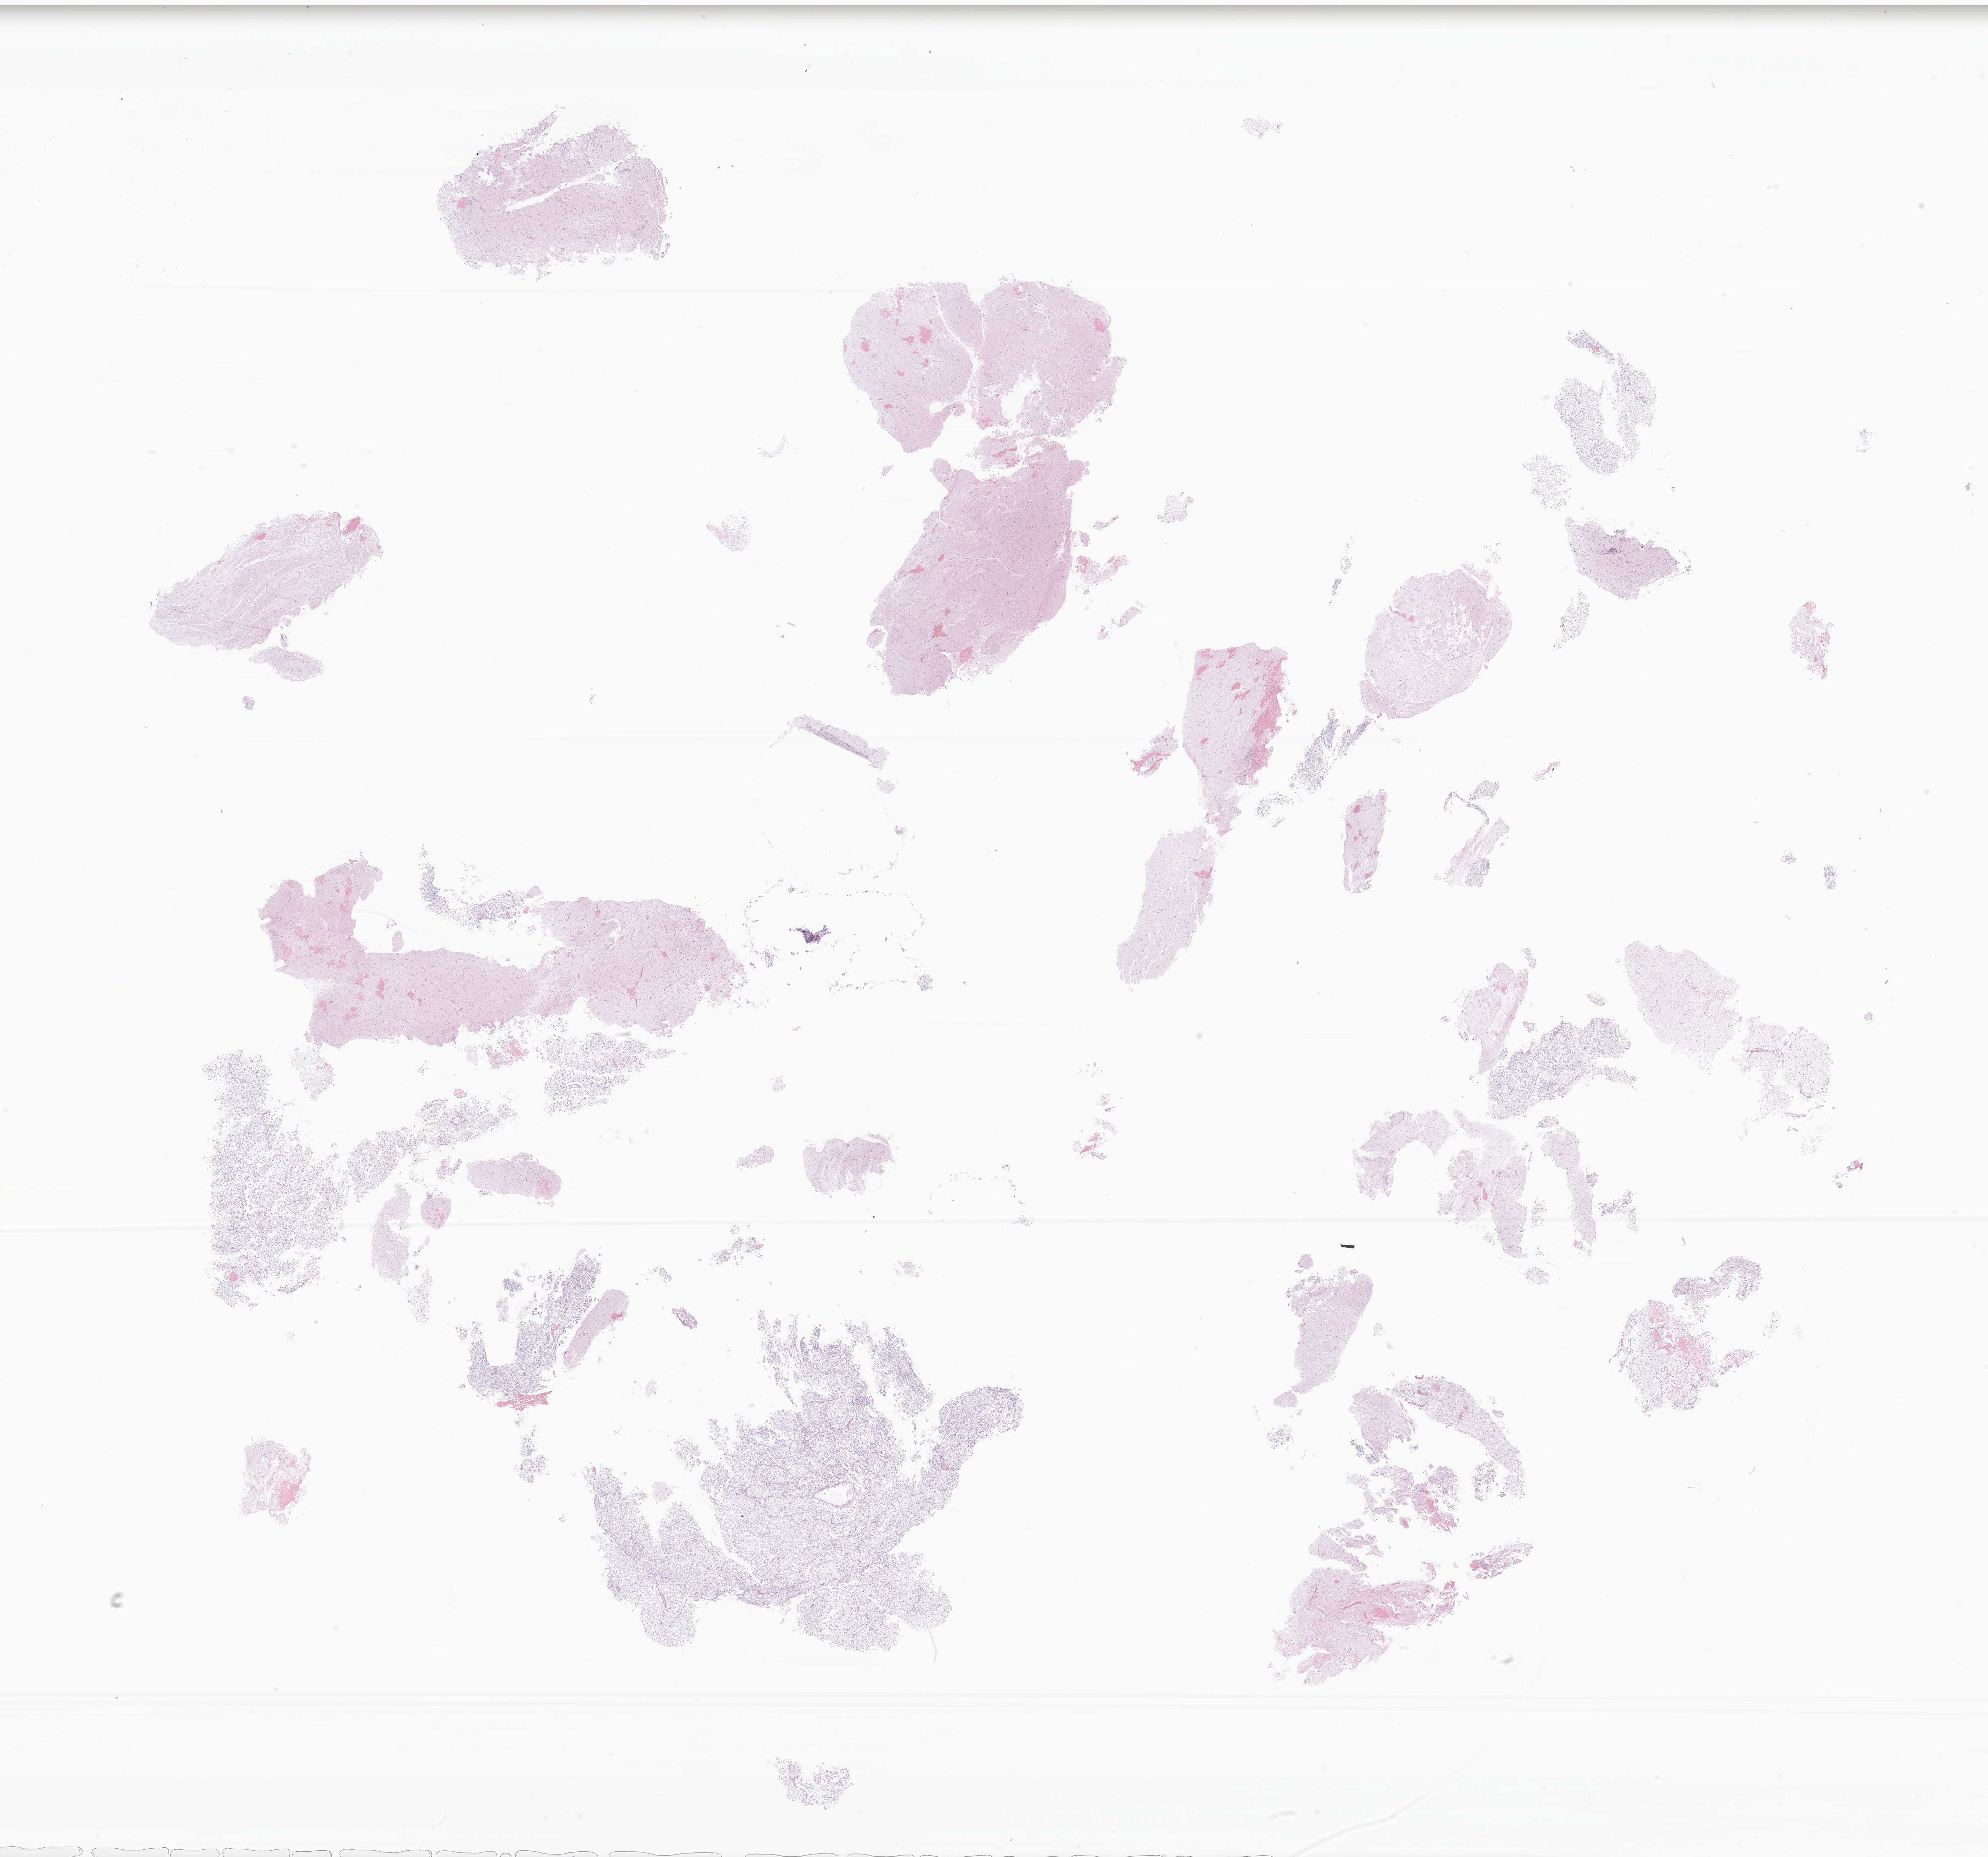
H&E whole-slide image of tumor tissue from the brain, low-resolution overview of the scanned area, about 24.9 x 23.3 mm, formalin-fixed, paraffin-embedded (FFPE) tissue. Patient: female, age 54 months (4 years 6 months).
• diagnosis: Glioma, malignant